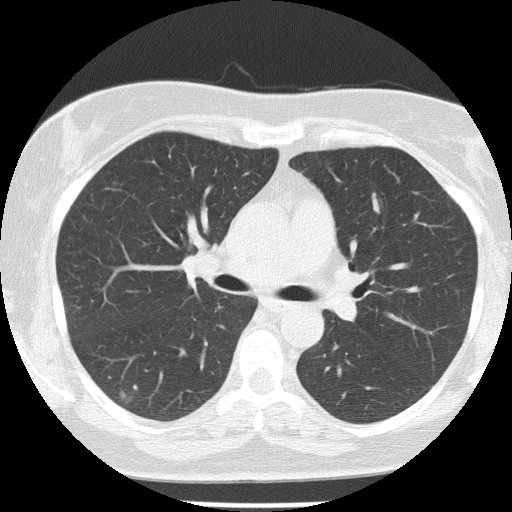
Axial slice from a low-dose chest CT screening exam. Baseline screening round. Lung window (W 1500 / L -600 HU). 2 mm slice thickness. Lung (sharp) reconstruction kernel (FC51). Slice 61 of 142 in the series. Female participant, aged 58 years at enrolment. Former smoker at enrolment.
- Expert reader's lesion annotation, bounding box (x1, y1, x2, y2) in pixels: (96, 368, 152, 424).
- The screening reader recorded 2 non-calcified nodules or masses ≥4 mm on this exam; which of them this box marks is not recorded.